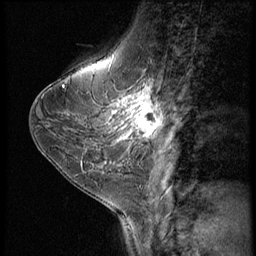
Breast MRI (dynamic contrast-enhanced), one sagittal slice. Position 21 of 56 along the scan axis. Dynamic contrast-enhanced series, image 2 of 3 at this slice position (ordered by acquisition). 1.5 T. TE 4.2 ms, TR 9 ms. 256 × 256 image matrix. Patient: female, 38 years. Case-level facts recorded for this patient, not image findings: setting: breast cancer imaged before/during neoadjuvant chemotherapy; receptor status: triple-negative.
Structures marked on this image (semi-automatic segmentation, software-assisted and operator-edited):
- analysis volume of interest (the breast-tissue region the enhancement analysis was run in; not a lesion): bounding box <107,95,167,149> (left, top, right, bottom; pixels)
- tumour enhancement mask (voxels above the 140 % enhancement threshold inside the analysis volume of interest): <109,95,163,139>